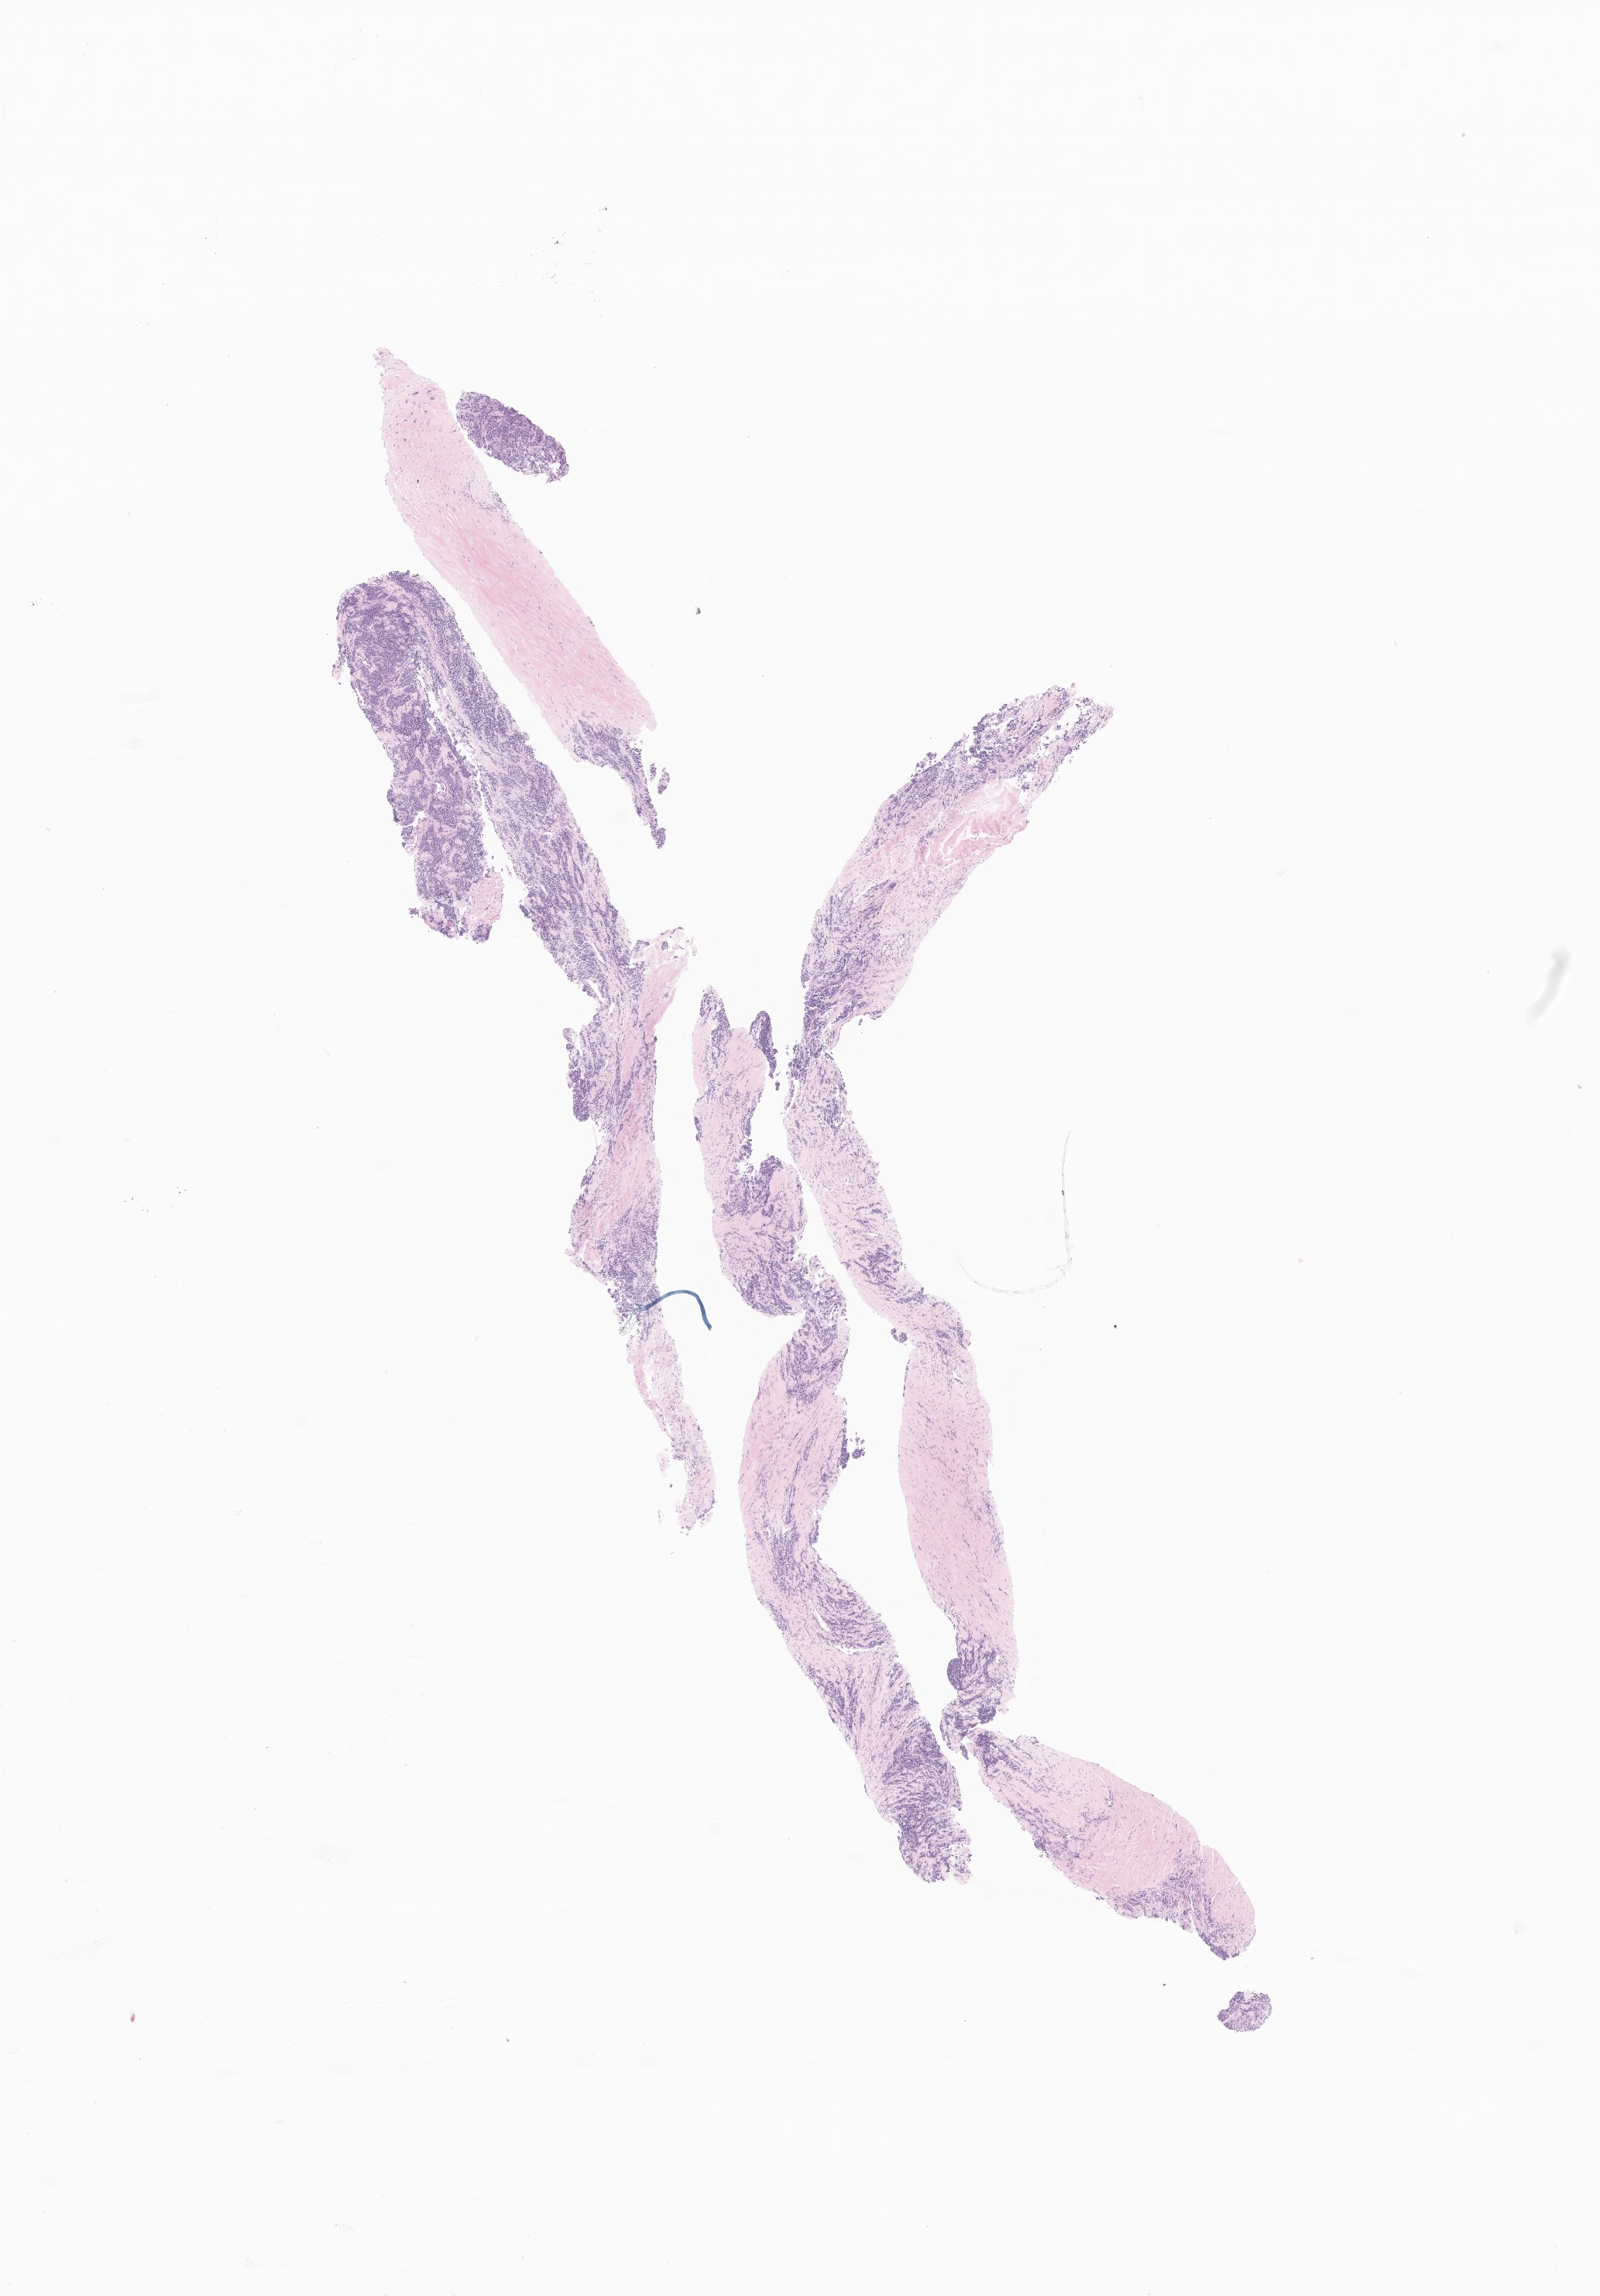
Digitized hematoxylin and eosin (H&E)-stained section of tumor tissue from the upper limb, a low-resolution overview of the entire scanned area, about 8.7 x 12.5 mm. FFPE section. Patient: male, age 178 months (14 years 10 months).
Diagnosis (ICD-O-3 morphology term): Sarcoma, NOS.